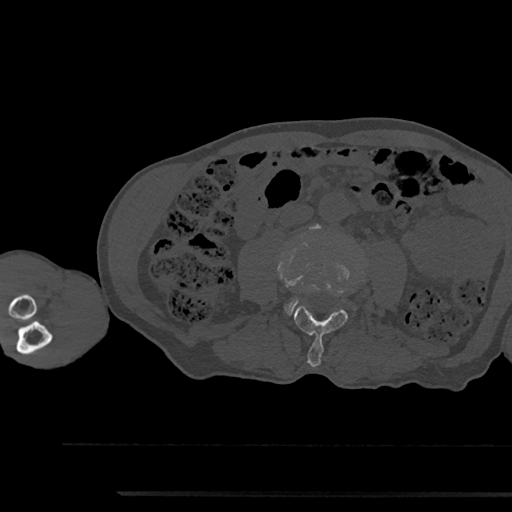
CT including the spine, one axial slice; position 458 of 797 along the scan axis; reconstruction kernel Br40s/3; 120 kVp; bone window (W 1800 / L 400 HU); 0.5 mm slice thickness; 512 × 512 image matrix, field of view 367 × 367 mm. Patient: male, 79 years. Case-level facts recorded for this patient, not image findings: primary cancer: prostate.
Outlined on this slice (semi-automatically segmented with operator editing):
- L3 vertebra: bounding box [x1, y1, x2, y2] px = [294, 306, 348, 367]
- L4 vertebra: [286, 299, 298, 315]